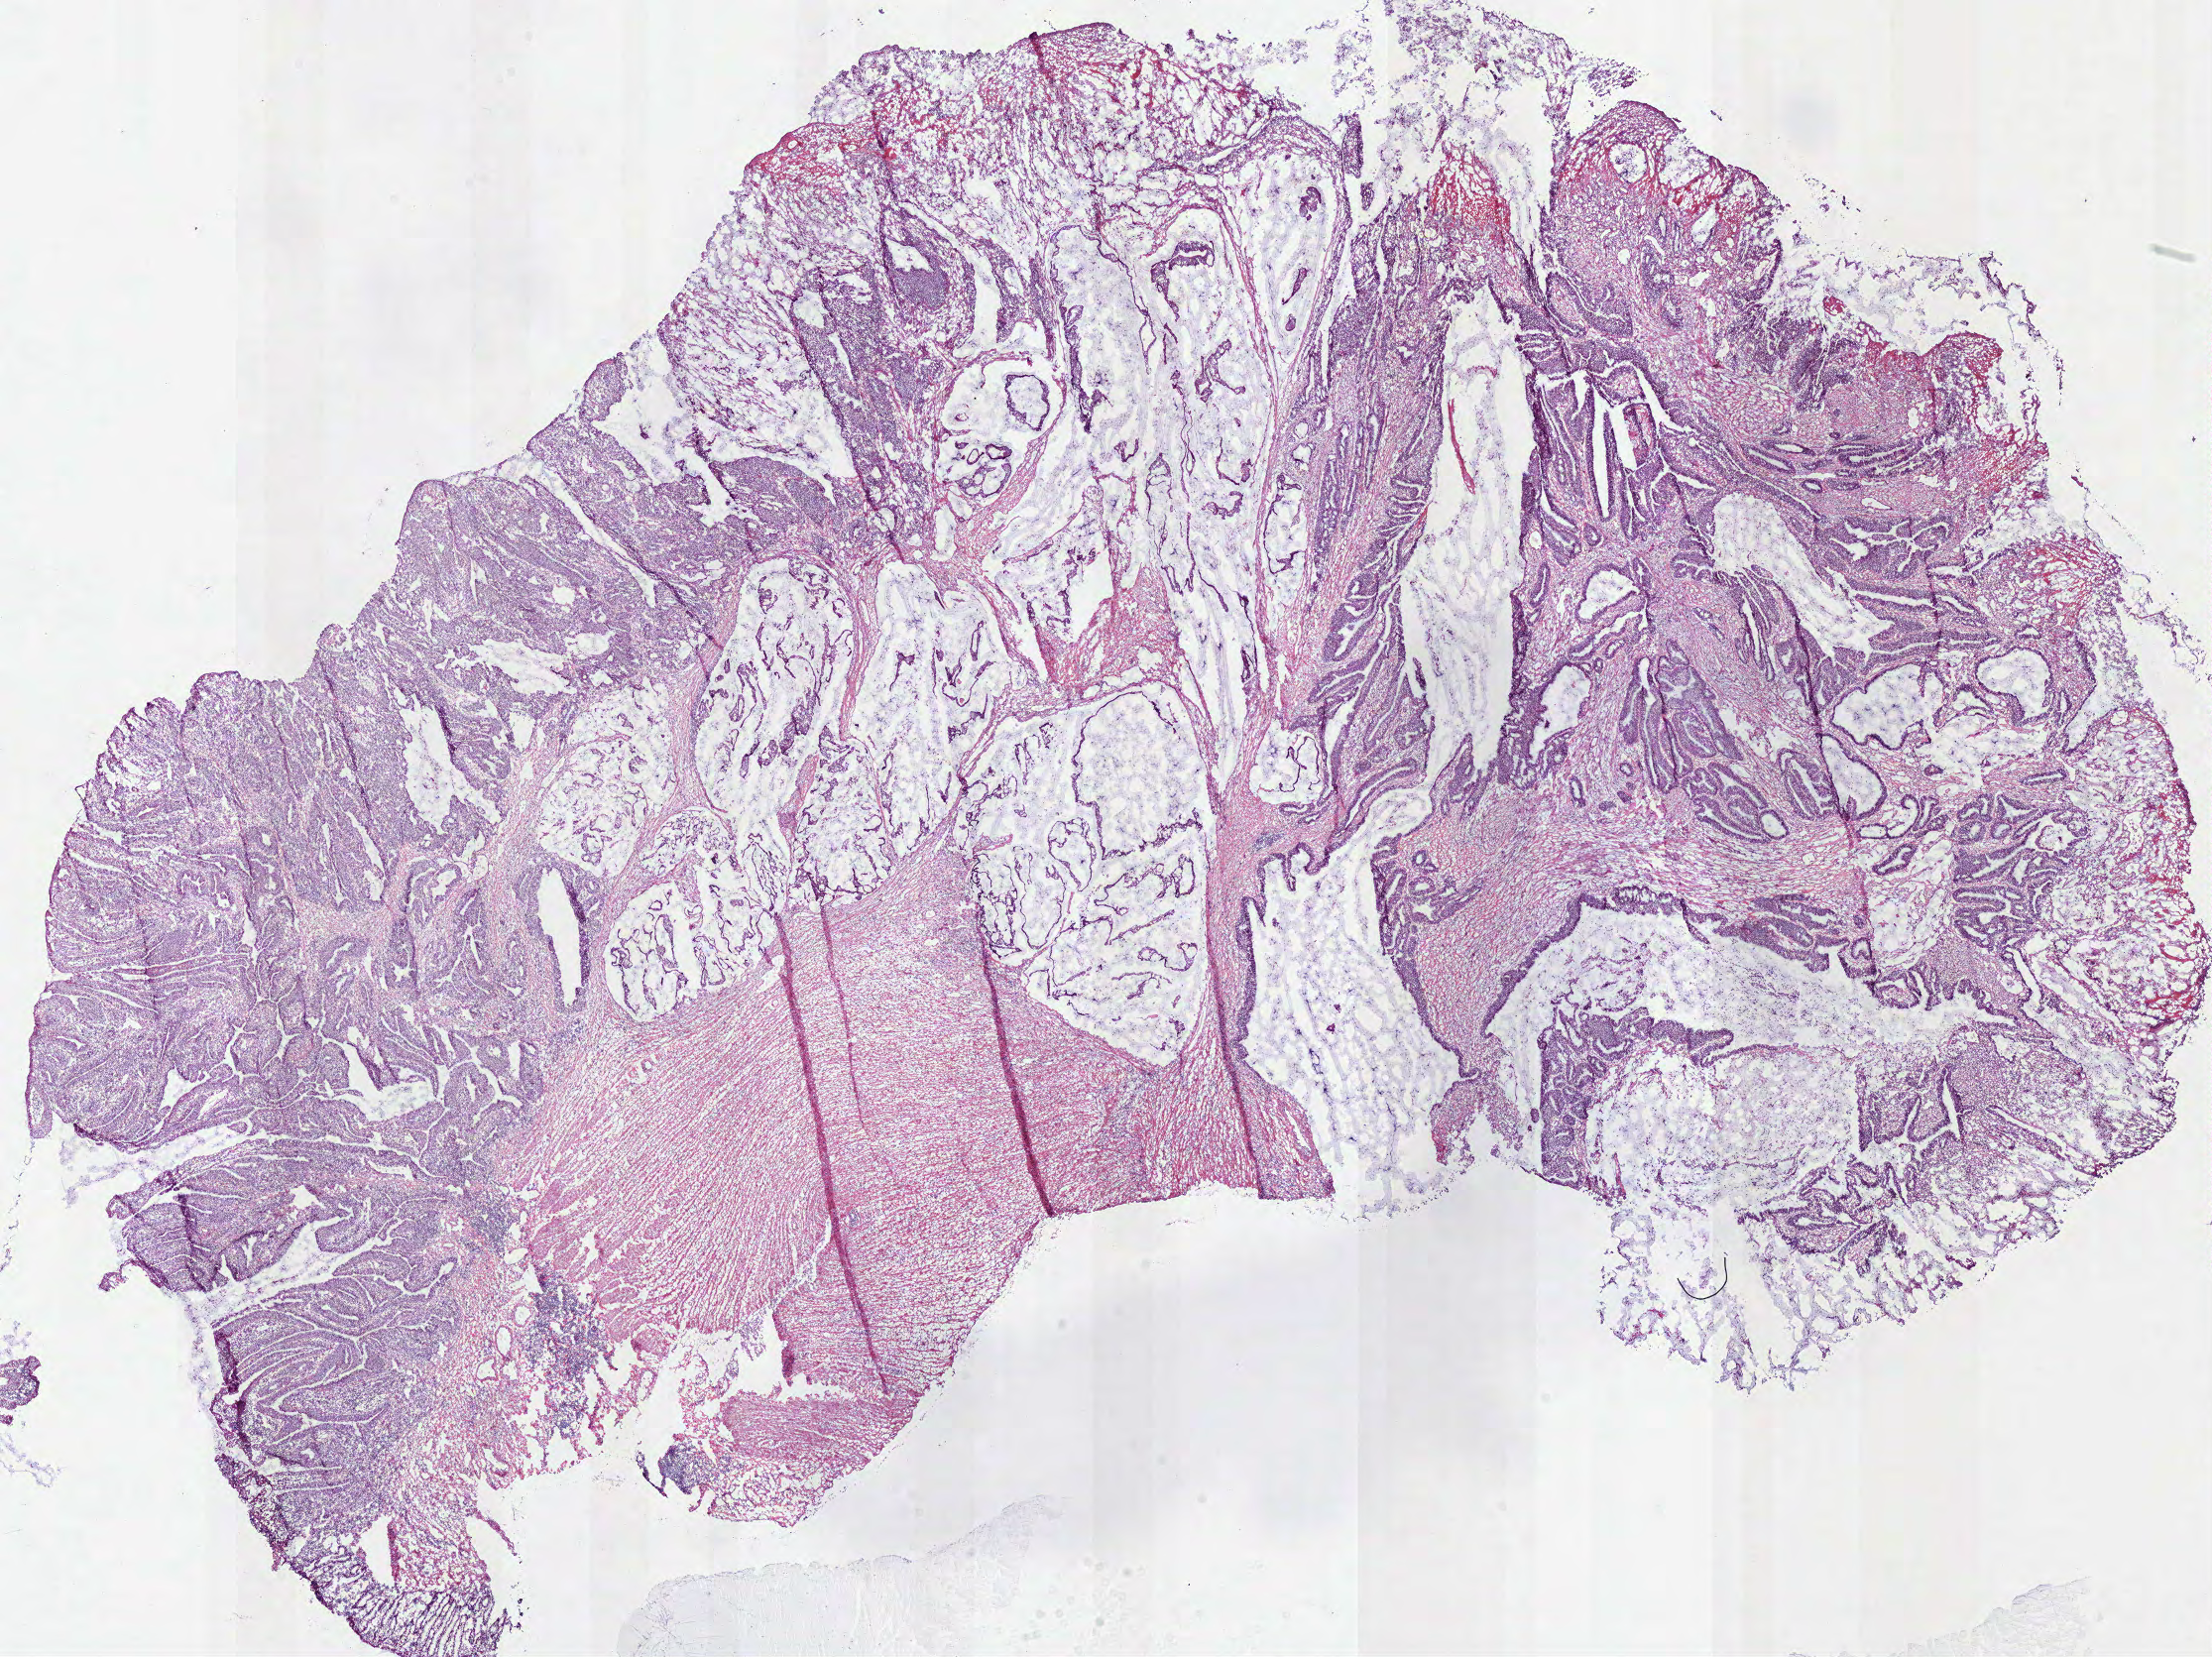
H&E whole-slide image, shown as a low-resolution overview of the whole scanned area (about 17.6 x 13.2 mm, slide scanned at 40x), frozen section, primary tumour sample from the colon. Male patient; age at initial diagnosis 45 years. Slide review estimates, as recorded: tumour cells 83%, tumour nuclei 80%, normal cells 0%, stromal cells 15%, necrosis 2%.
Diagnosis: Mucinous adenocarcinoma (cecum). AJCC pathologic stage: I.